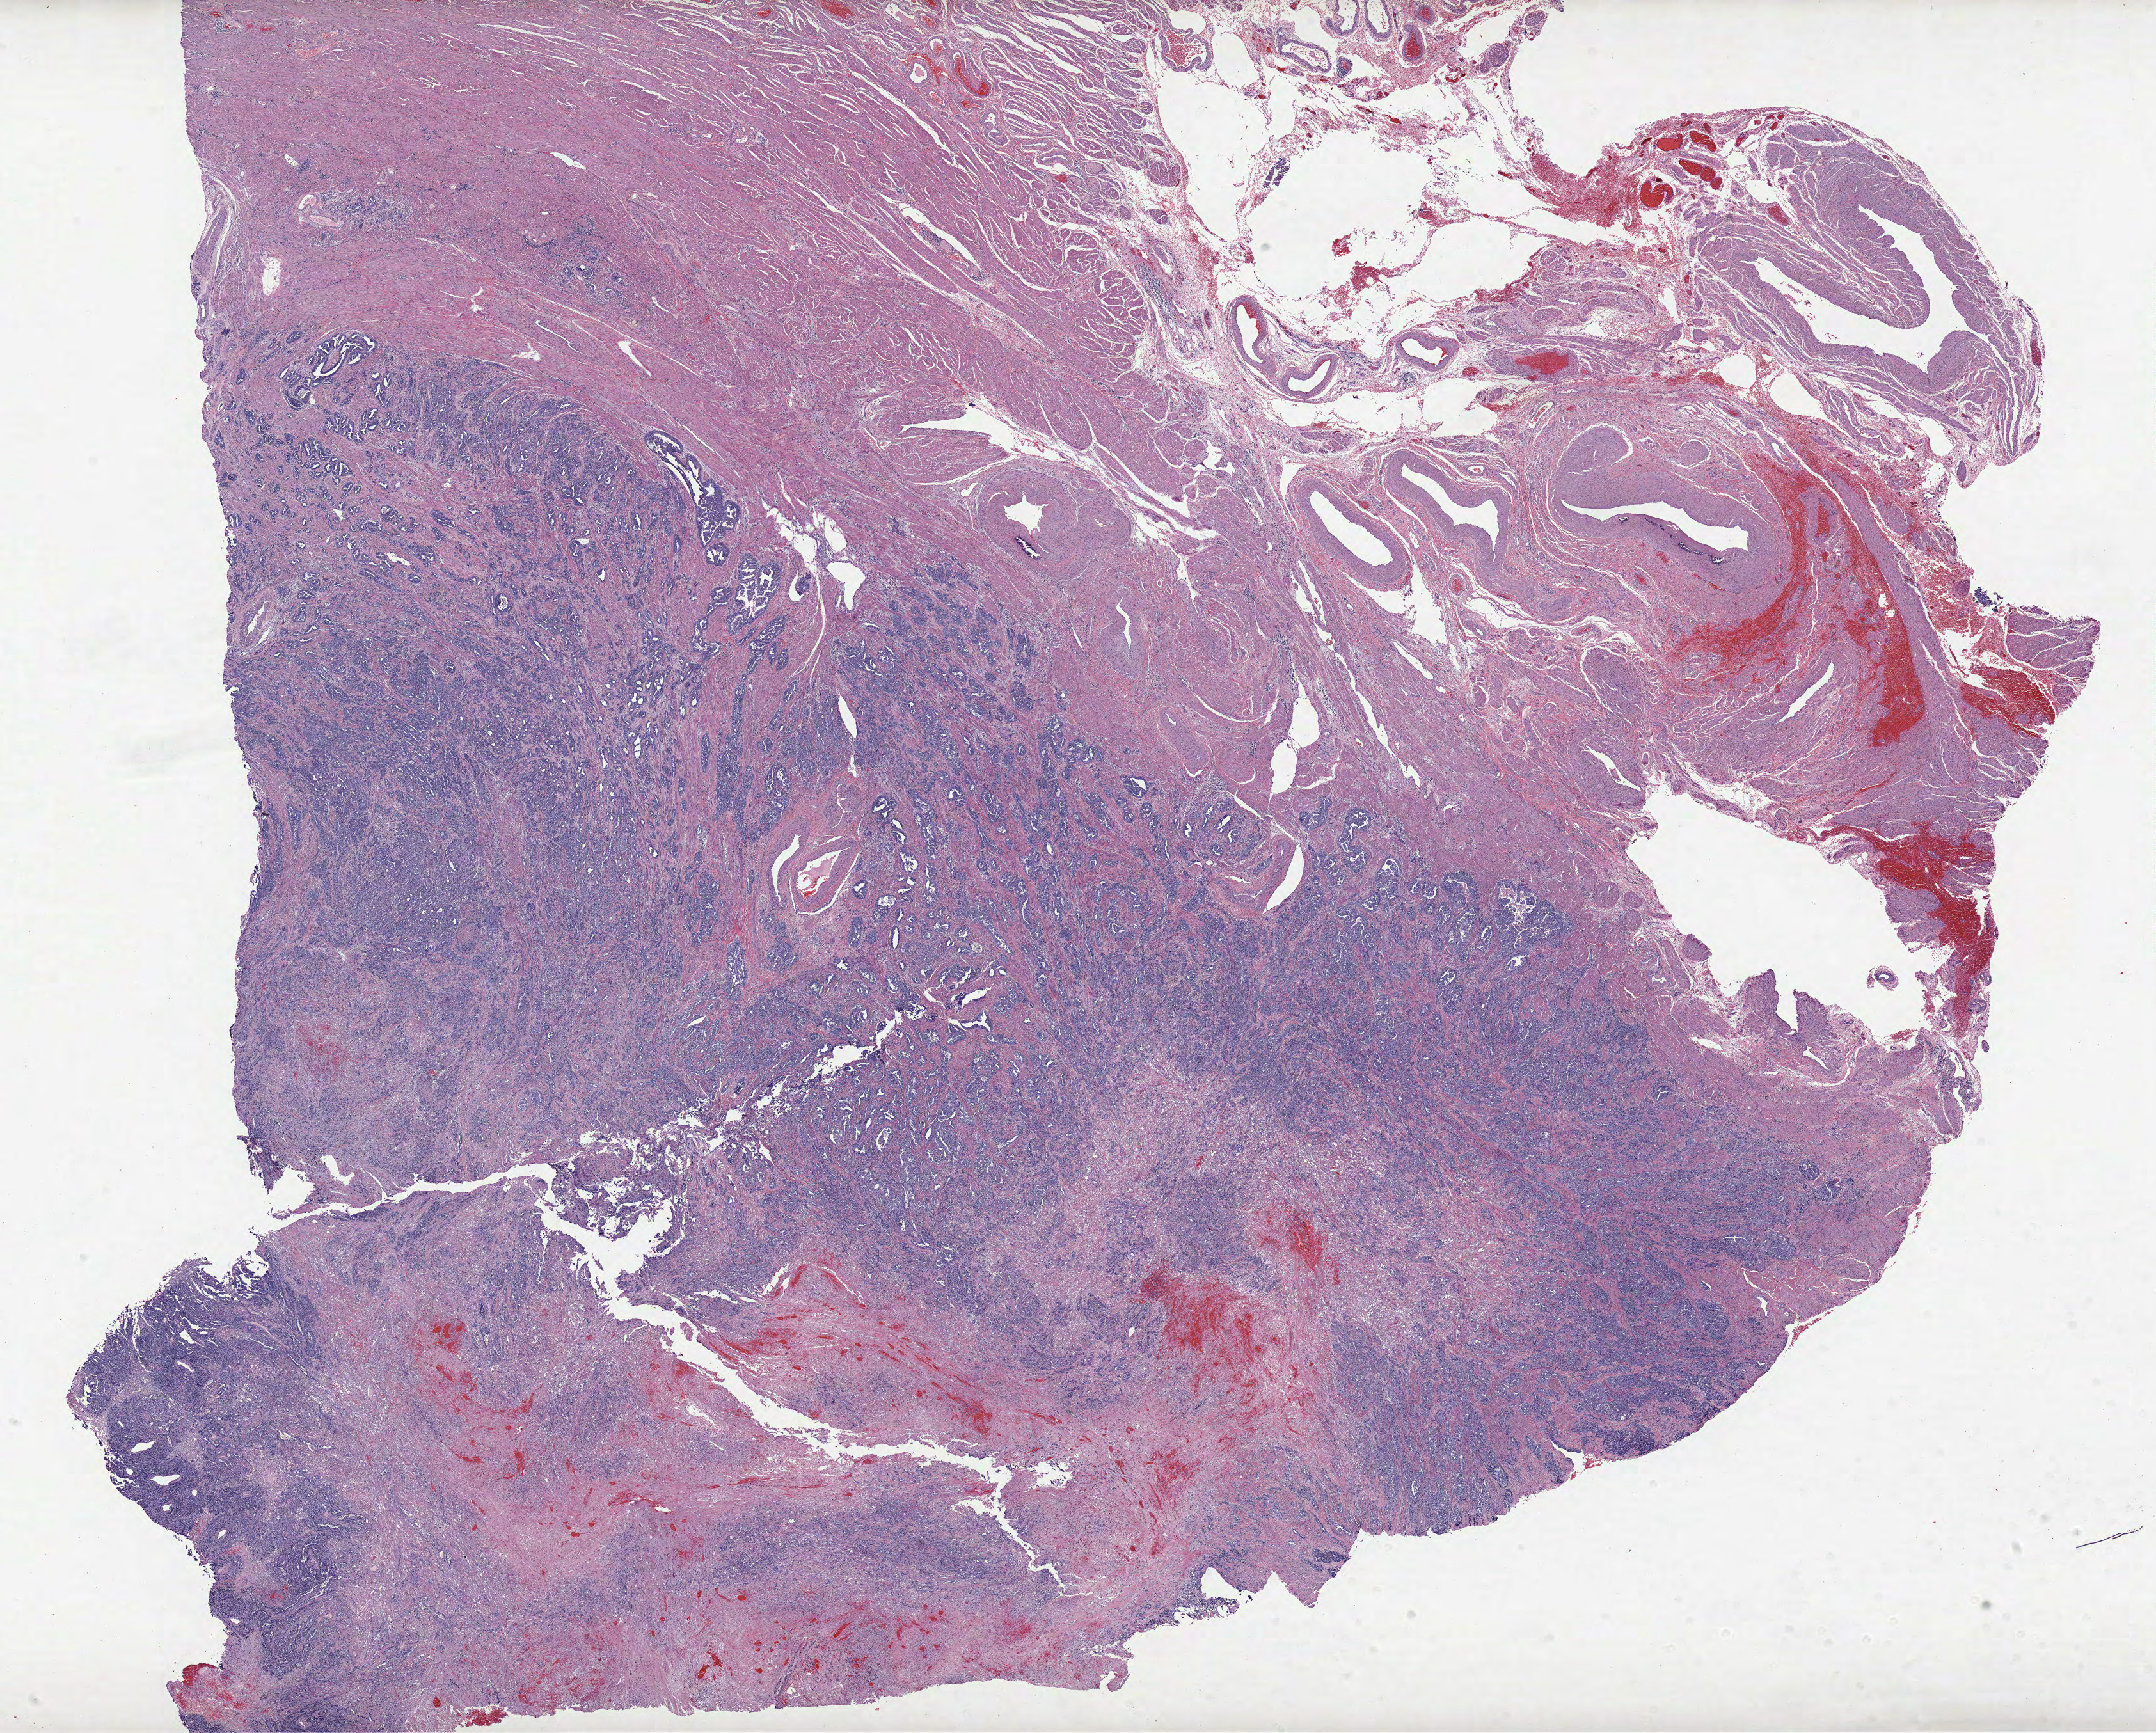
H&E whole-slide image — a low-resolution overview of the entire scanned area, about 26.9 x 21.6 mm (acquisition: 20x scan); FFPE section; sample: primary tumour, uterus. Female patient; age at initial diagnosis 70 years. Histologic grade: G3 (poorly differentiated).
• diagnosis: Serous cystadenocarcinoma, NOS (endometrium)
• FIGO stage: IIIC2